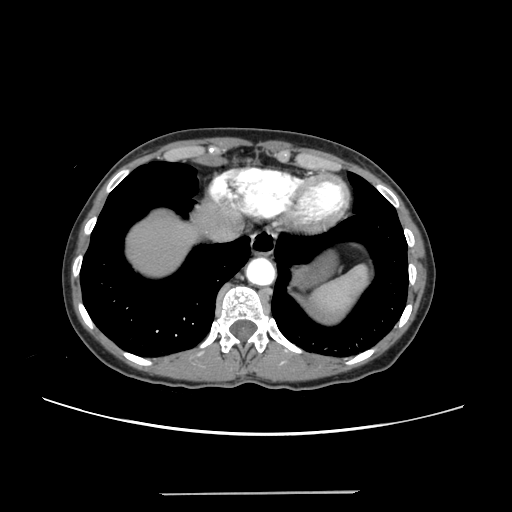
Contrast-enhanced abdominal CT, one axial slice; slice 221 of 240 in the series (ordered by position); 120 kVp; soft-tissue window (W 400 / L 40 HU); 512 × 512 image matrix. Female patient, age 60 years. From the clinical record (not read from this slice): diagnosis: colorectal cancer liver metastases, imaged before liver resection; multiple liver metastases: no; largest metastasis: 1.5 cm; chemotherapy before resection: yes.
Outlined on this slice (expert manual segmentation):
- liver: bounding box [x1, y1, x2, y2] px = [127, 207, 220, 277]
- planned liver remnant (the part of the liver to remain after resection): [127, 207, 220, 277]